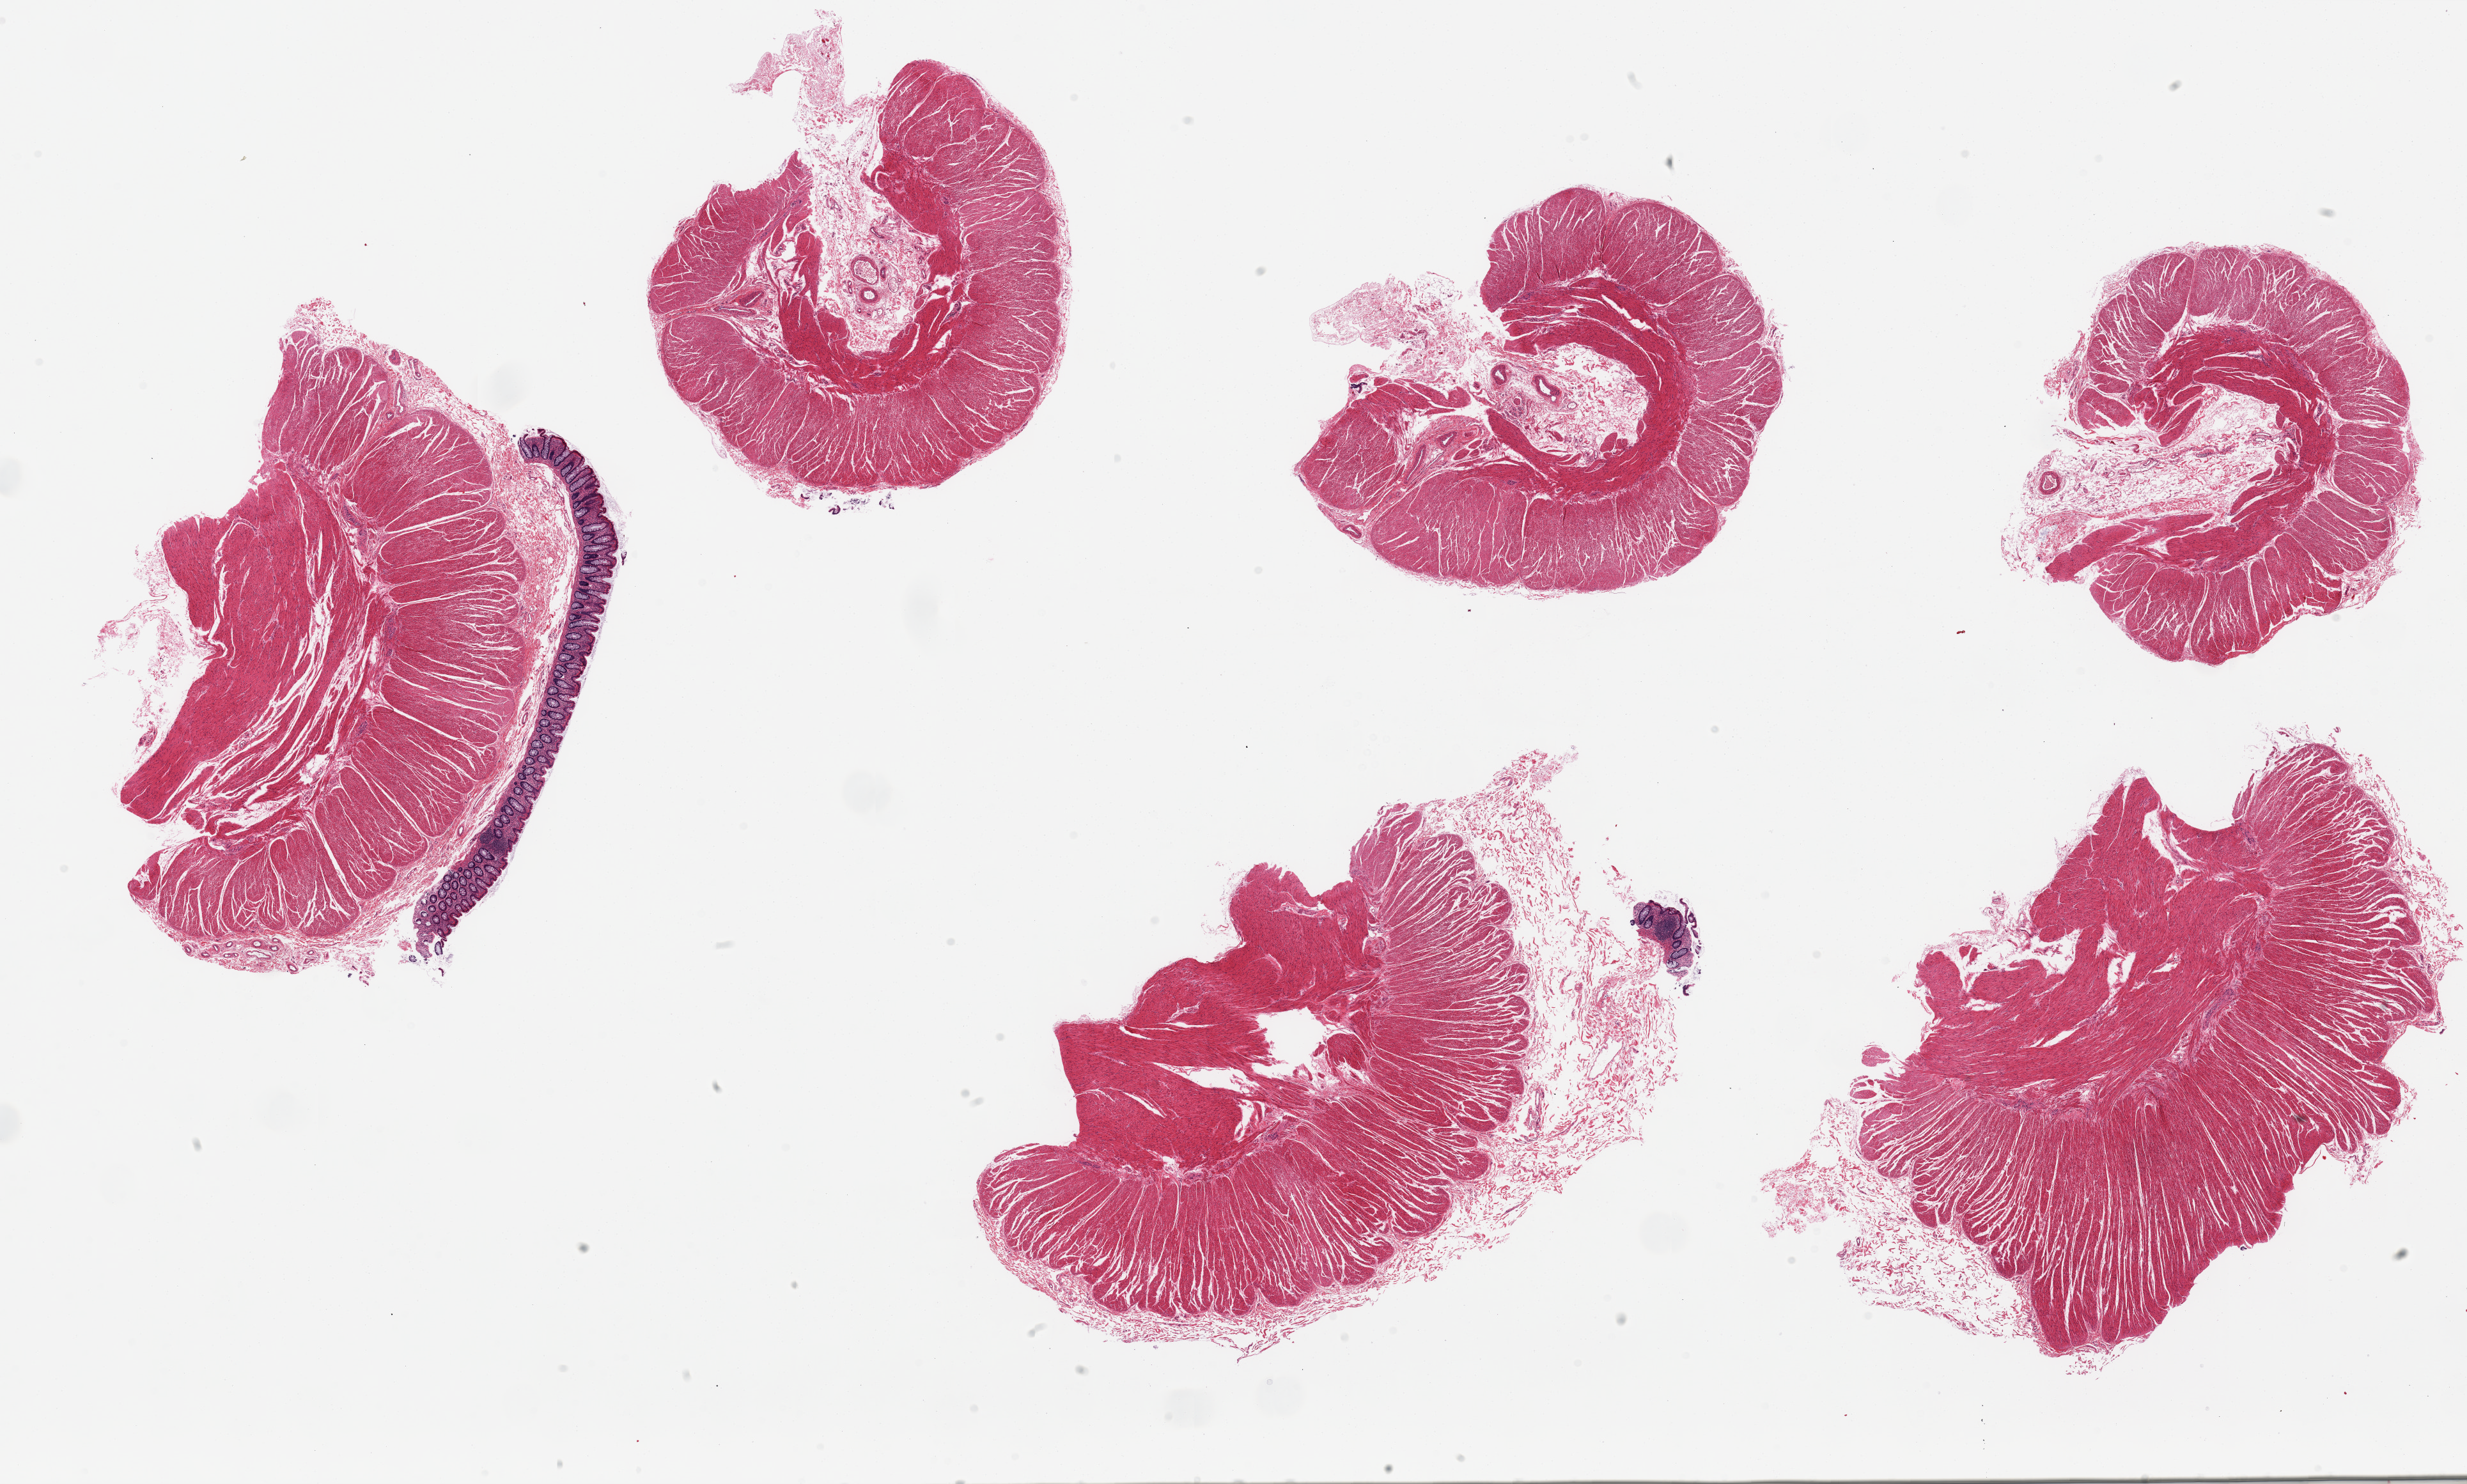
Haematoxylin and eosin whole-slide image, brightfield, whole scanned area (about 30.5 x 18.4 mm) shown as a low-resolution overview. PAXgene-fixed paraffin-embedded (PFPE) section. Target tissue: sigmoid colon. Tissue donor sample. Donor: female.
Review note (as recorded): 6 pieces, 2 pieces include mucosa (not target).